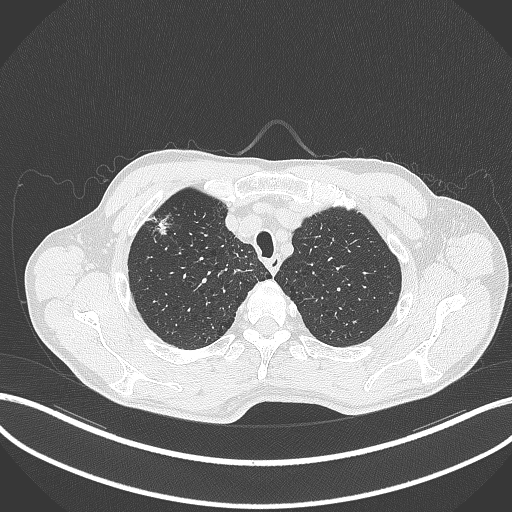
Chest CT, one axial slice; slice 357 of 427 in the series (ordered by position); reconstruction kernel B70f; 120 kVp; lung window (W 1500 / L -600 HU); 1 mm slice thickness; 512 × 512 image matrix, field of view 400 × 400 mm. Patient: male, 69 years. Case-level facts recorded for this patient, not image findings: clinical TNM (as recorded): T1b N1 M0.
Outlined on this slice (bounding box drawn by a radiologist):
- lung tumour (recorded histology: adenocarcinoma): box from (x=151, y=211) to (x=178, y=236) px